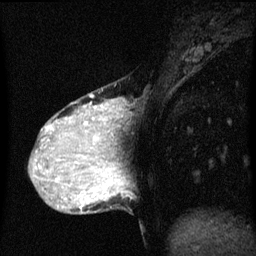
Breast MRI (dynamic contrast-enhanced), one sagittal slice. Position 17 of 60 along the scan axis. Dynamic contrast-enhanced series, image 2 of 3 at this slice position (ordered by acquisition). 1.5 T. TE 4.2 ms, TR 8 ms. 2 mm slice thickness. 256 × 256 image matrix, field of view 200 × 200 mm. Female patient, age 36 years.
Outlined on this slice (semi-automatically segmented with operator editing):
- analysis volume of interest (the breast-tissue region the enhancement analysis was run in; not a lesion): bounding box [x1, y1, x2, y2] px = [33, 88, 119, 169]
- tumour enhancement mask (voxels above the 70 % enhancement threshold inside the analysis volume of interest): [36, 100, 118, 169]